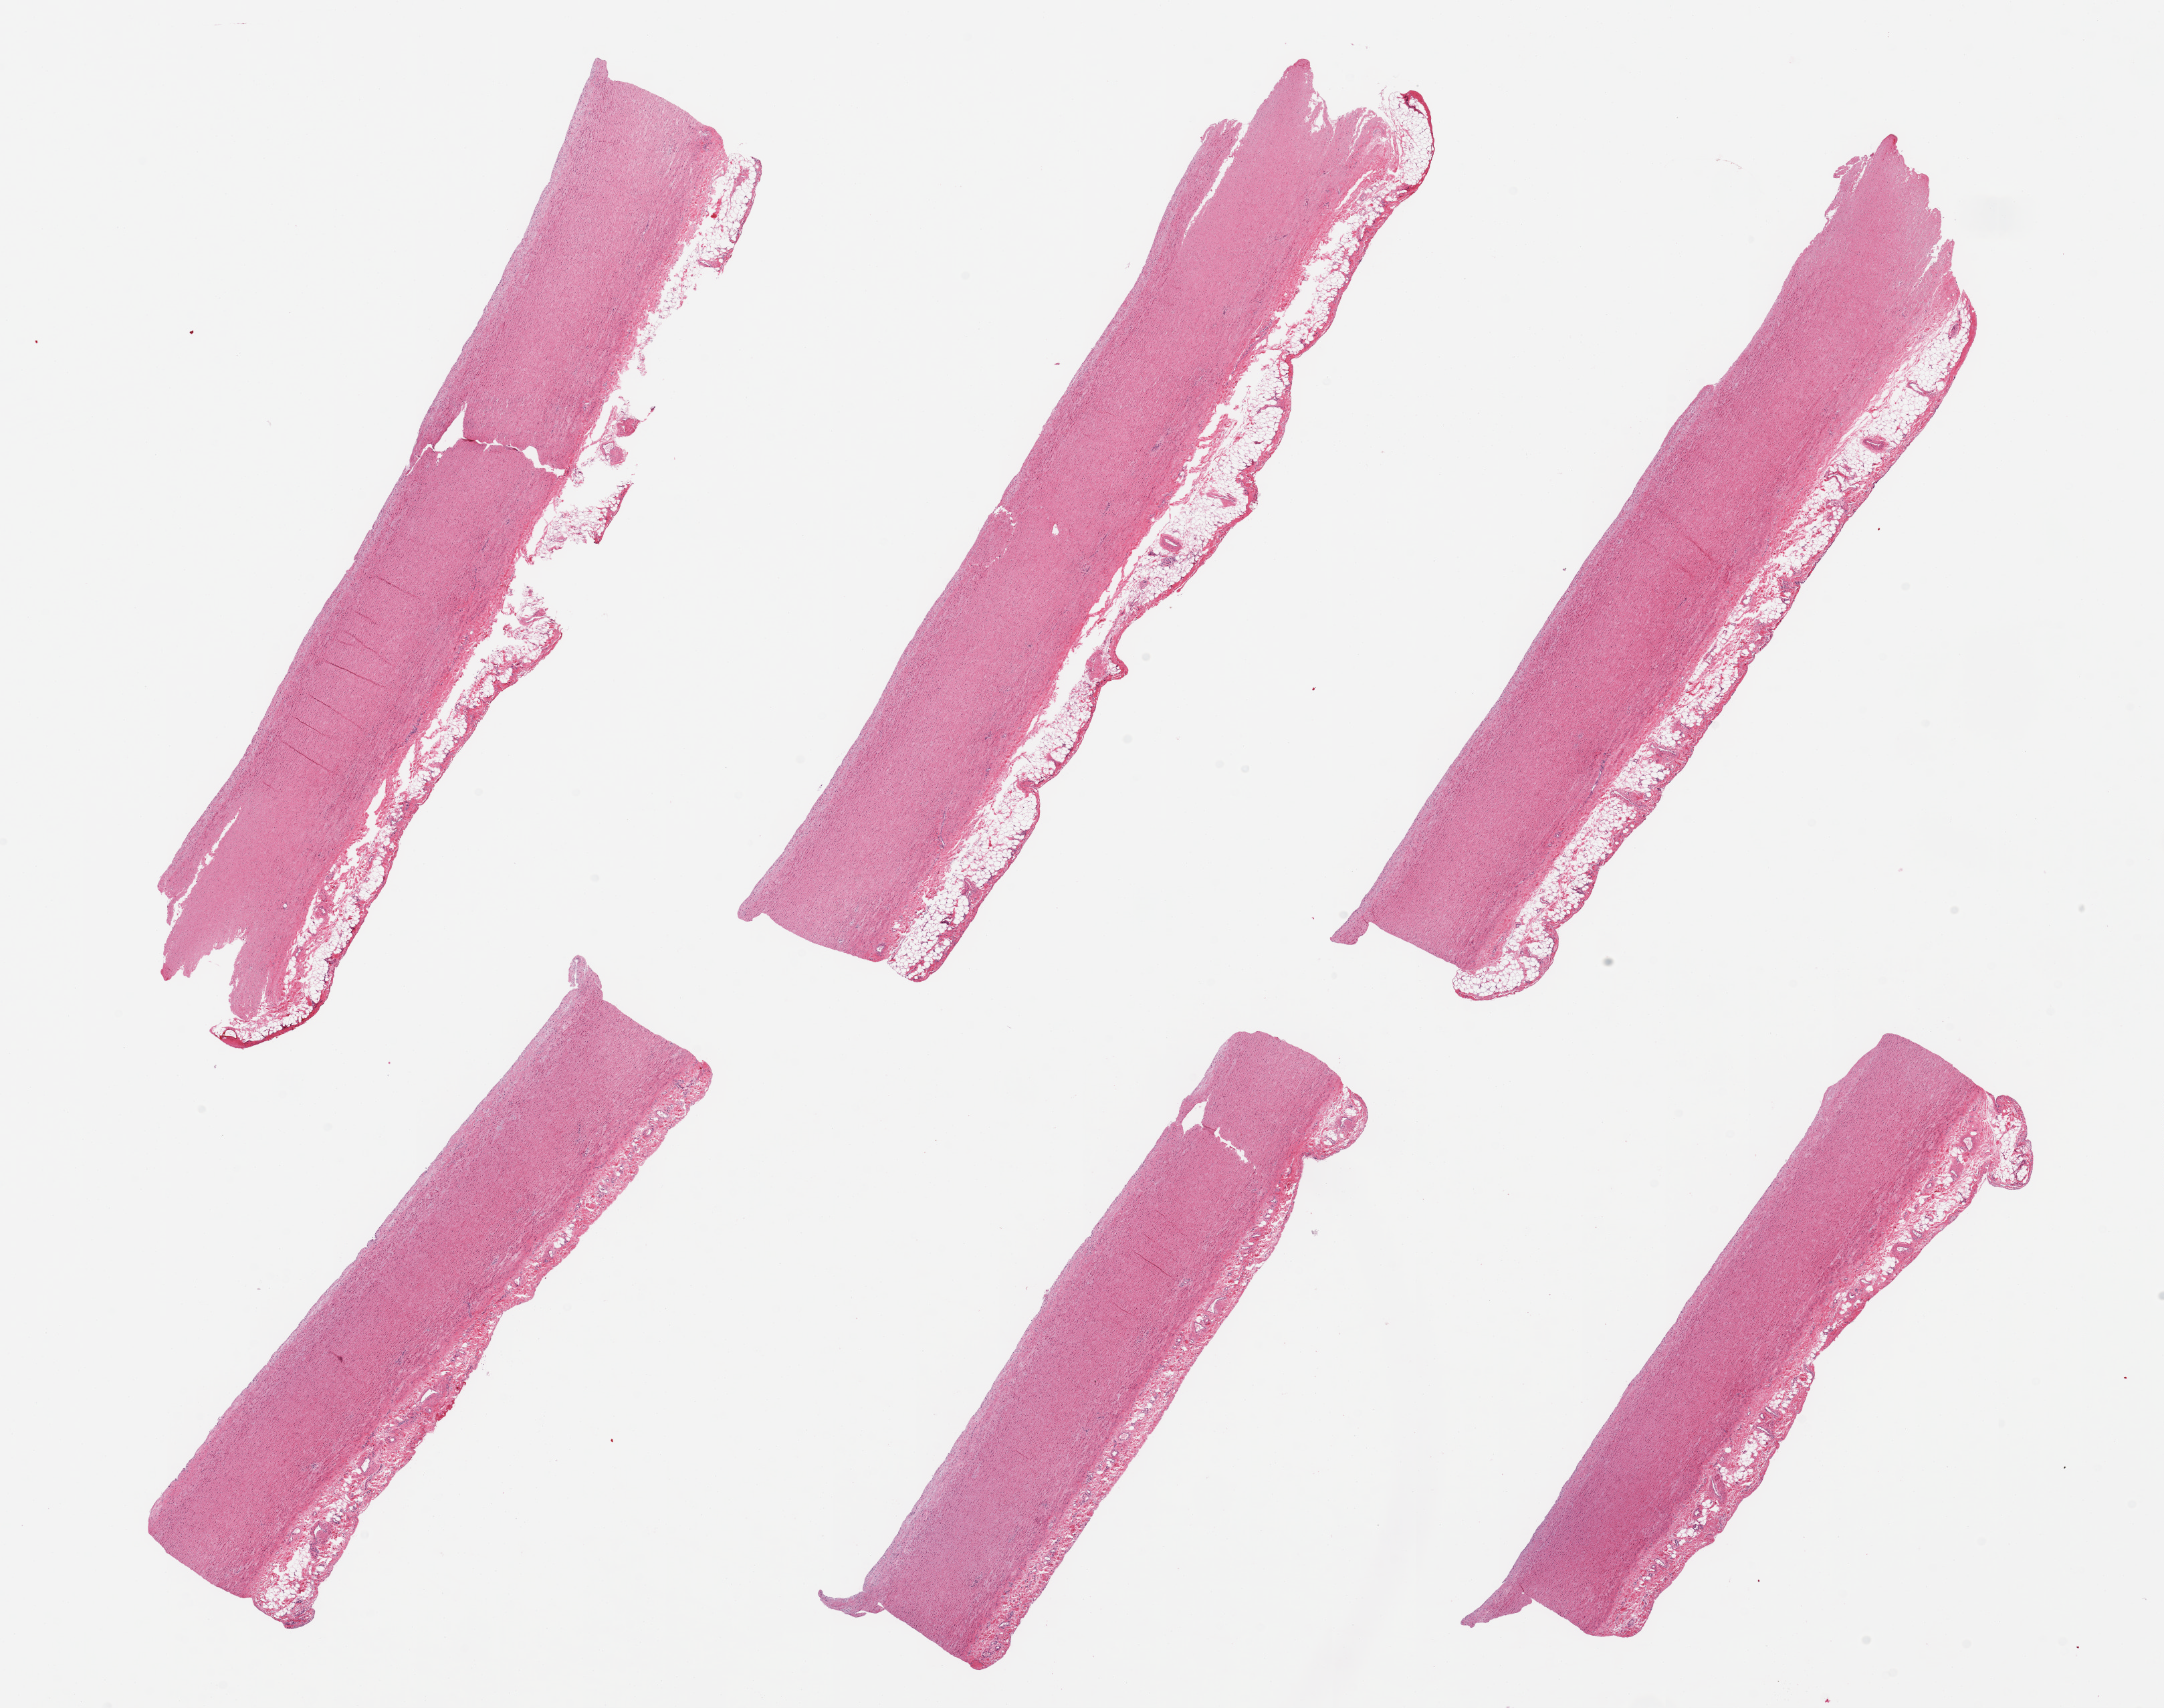
Whole-slide image, hematoxylin and eosin (H&E) stain — whole scanned area (about 25.6 x 20.2 mm, slide scanned at 20x) shown as a low-resolution overview, PAXgene-fixed, paraffin-embedded tissue, target tissue: aorta, donor tissue sample. Male donor.
* review note (as recorded): 6 pieces; all include residual attached fat/adventitia